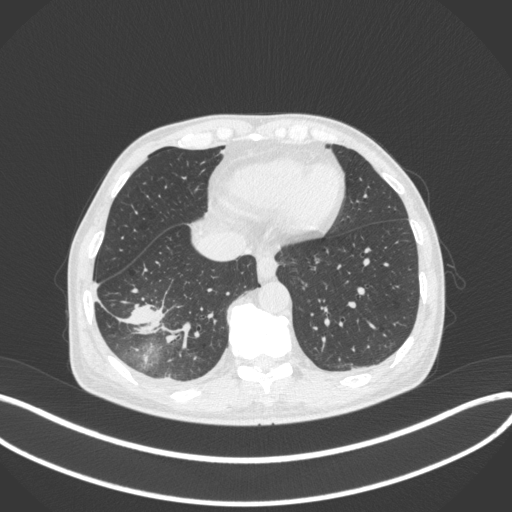
Chest CT, one axial slice. Reconstruction kernel B31f. 120 kVp. Lung window (W 1500 / L -600 HU). 1 mm slice thickness. 512 × 512 image matrix, field of view 400 × 400 mm. Male patient, age 64 years. From the clinical record (not read from this slice): clinical TNM (as recorded): T3 N0 M0; histopathological grade: G2-3.
Annotated regions visible in this slice (bounding box drawn by a radiologist):
- lung tumour (recorded histology: adenocarcinoma): bounding box <122,300,164,337> (left, top, right, bottom; pixels)